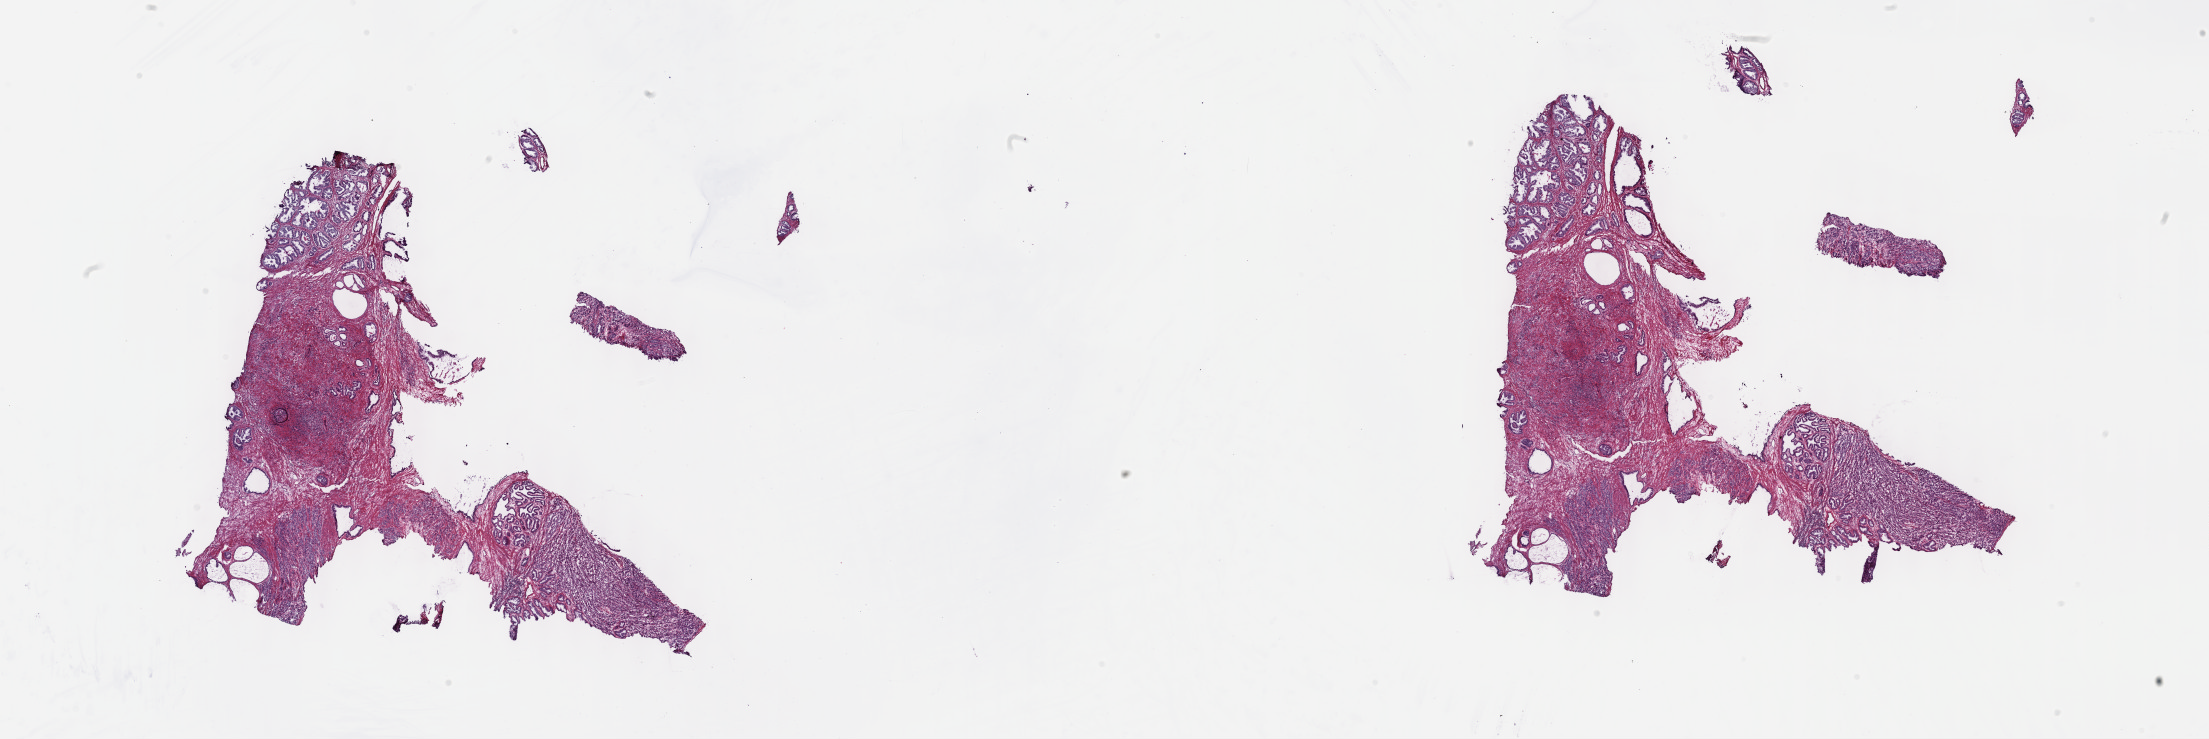
Hematoxylin and eosin (H&E) stained whole-slide image, a low-resolution overview of the entire scanned area, about 35.7 x 12.0 mm; frozen section from the top of the tissue portion; prostate, primary tumour sample. Male, age 67 years at initial diagnosis. Gleason score: 7 (4+3). Composition of this section per pathologist review: tumour cells 60%, tumour nuclei 60%, normal cells 15%, stromal cells 25%, necrosis 0%. Infiltration values recorded for this section: lymphocyte infiltration 3%, monocyte infiltration 1%, neutrophil infiltration 1%.
Lymph nodes positive (case pathology): 0 of 18 examined. Laterality: bilateral. Histologic diagnosis: Adenocarcinoma, NOS (prostate gland).